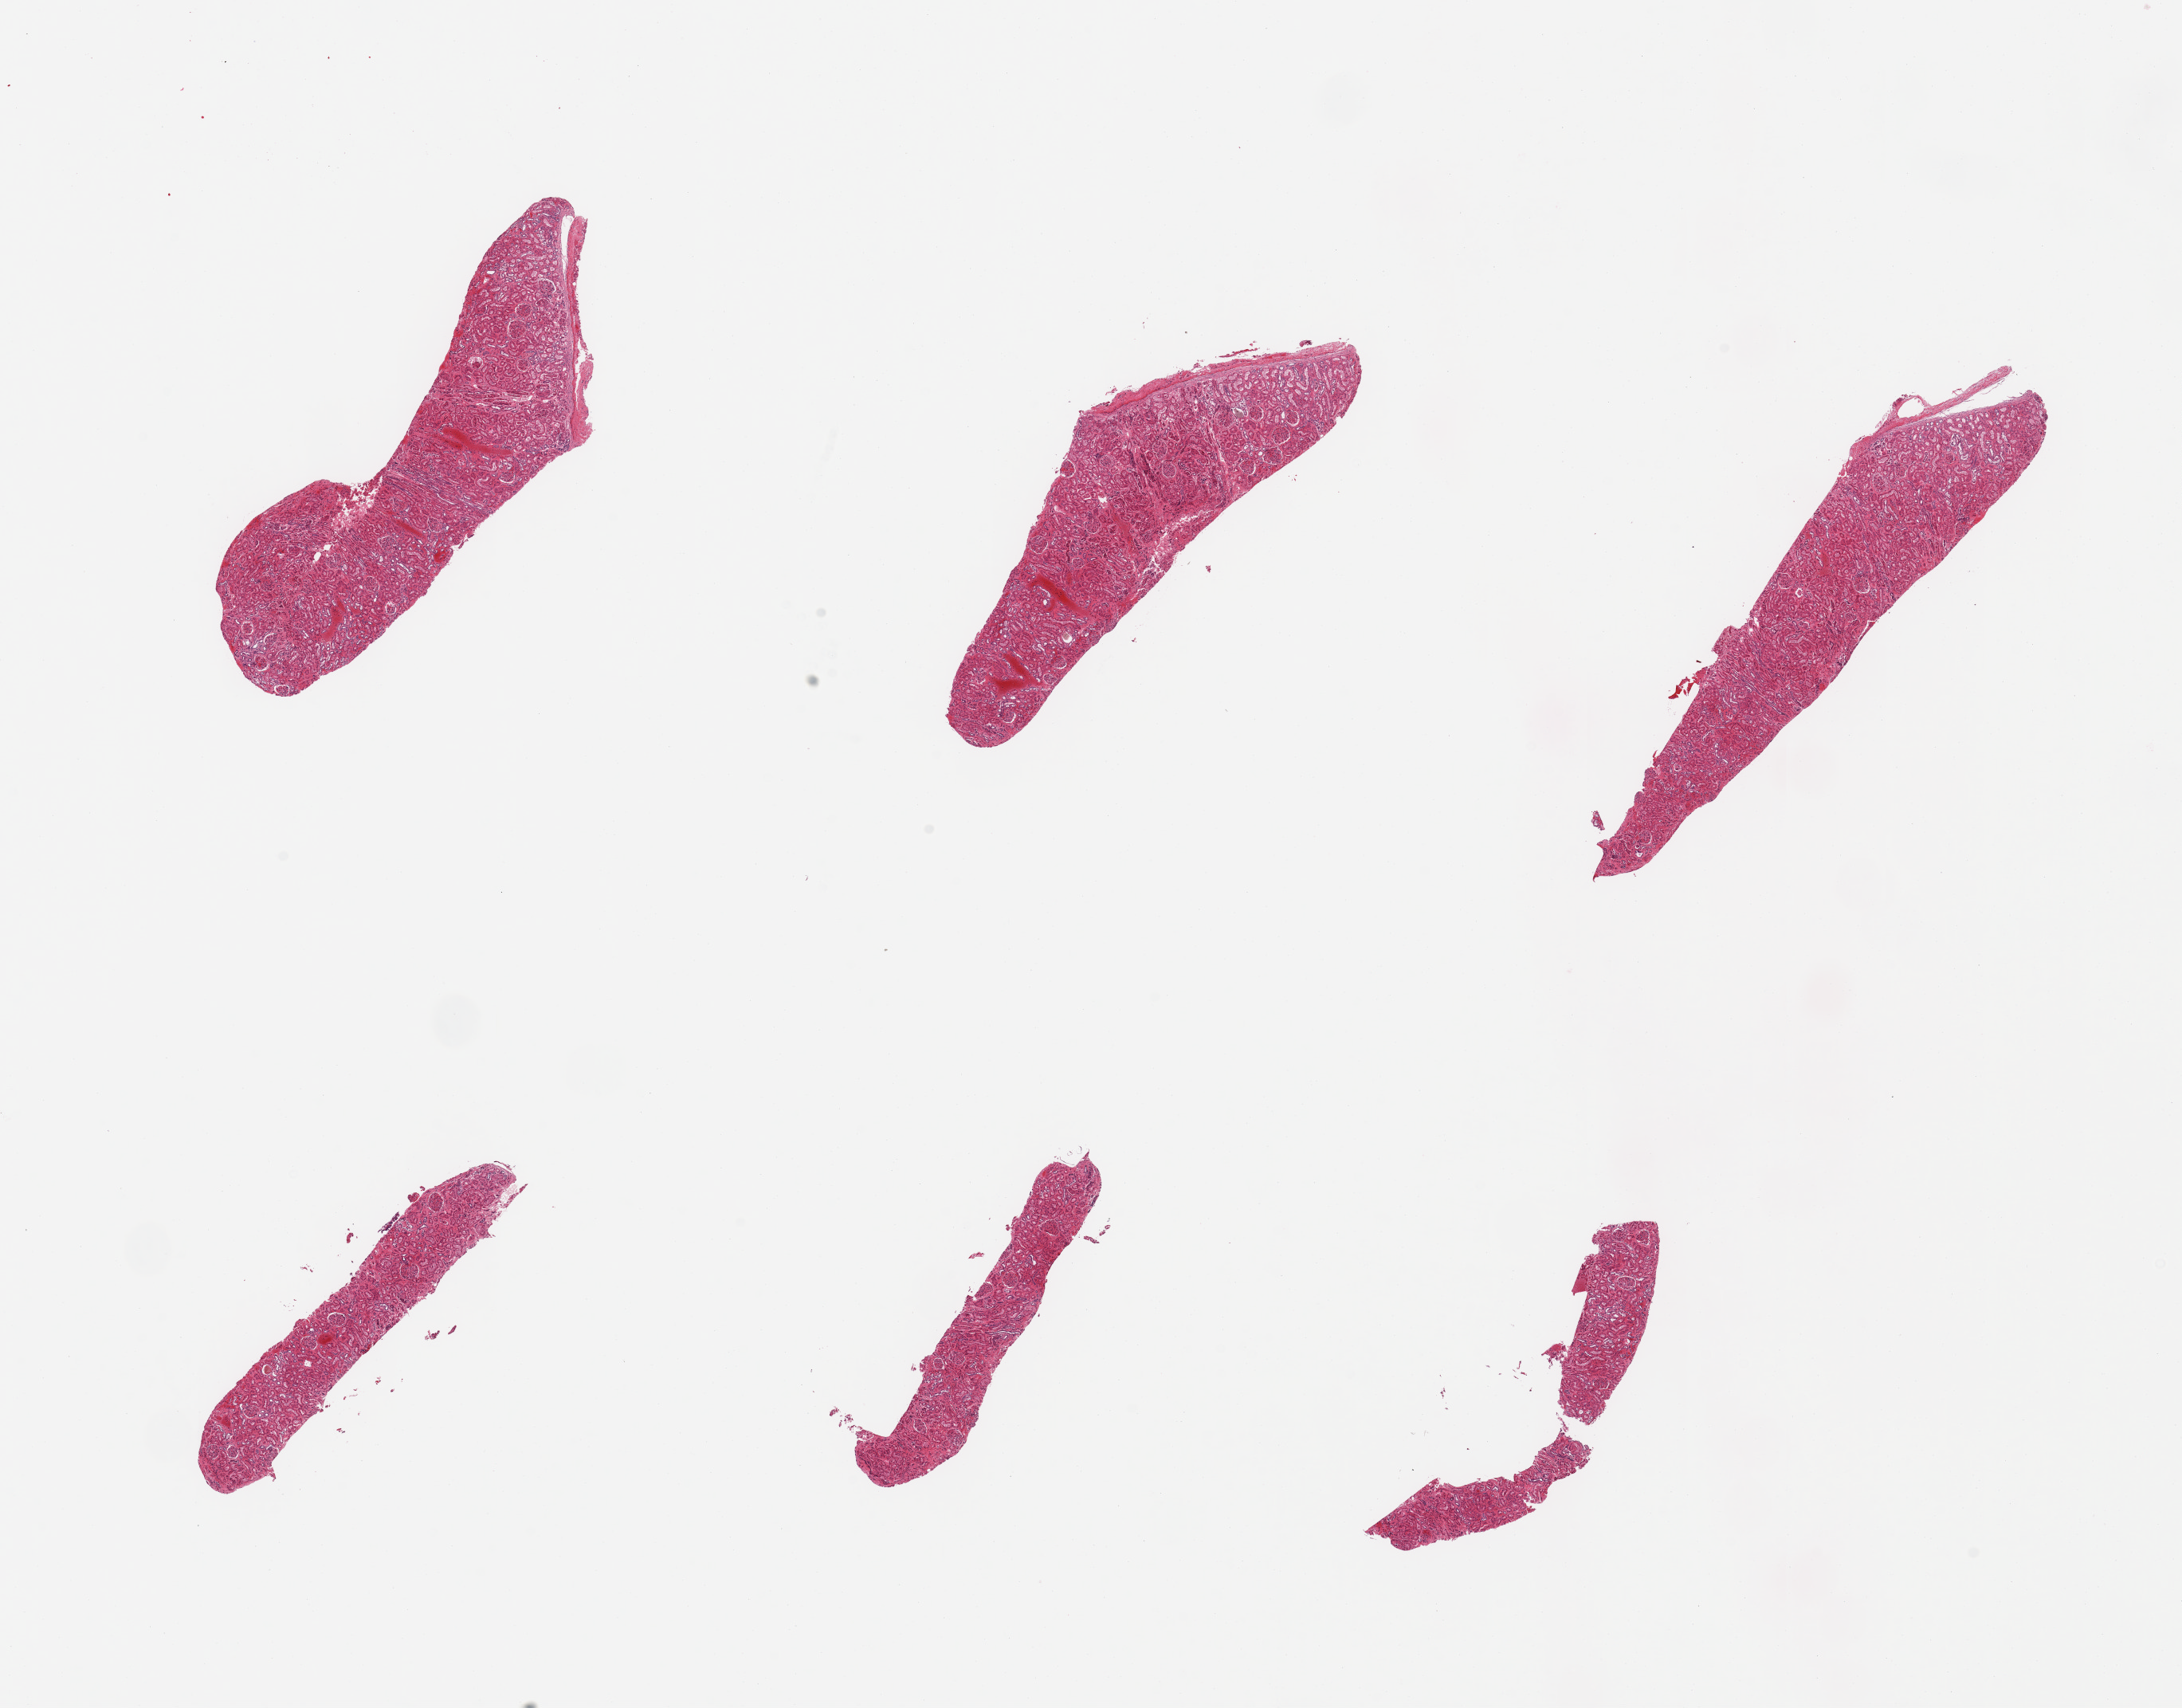
Hematoxylin and eosin (H&E) whole-slide image, brightfield — whole scanned area (about 21.7 x 17.0 mm, from a 20x scan) shown as a low-resolution overview, PAXgene-fixed, paraffin-embedded tissue, section of renal cortex (target tissue), donor tissue sample. Male donor.
Reviewer comment on this tissue sample: 6 pieces, glomeruli present; tubules mildy autolyzed.